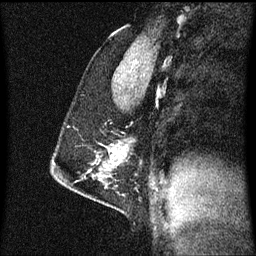
Breast MRI (dynamic contrast-enhanced), one sagittal slice; slice 38 of 60 in the series (ordered by position); dynamic contrast-enhanced series, image 2 of 3 at this slice position (ordered by acquisition); 1.5 T; TE 4.2 ms, TR 8.4 ms; 2 mm slice thickness; 256 × 256 image matrix, field of view 200 × 200 mm. Female patient, age 40 years. Case-level facts recorded for this patient, not image findings: setting: breast cancer imaged before/during neoadjuvant chemotherapy; receptor status: triple-negative.
Annotated regions visible in this slice (semi-automatic segmentation, software-assisted and operator-edited):
- analysis volume of interest (the breast-tissue region the enhancement analysis was run in; not a lesion): bounding box [x1, y1, x2, y2] px = [53, 126, 129, 195]
- tumour enhancement mask (voxels above the 70 % enhancement threshold inside the analysis volume of interest): [117, 160, 120, 163]